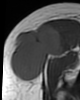
MRI of an extremity soft-tissue mass, one axial slice. Slice 25 of 46 in the series (ordered by position). MR volume resampled by the dataset authors to the PET/CT grid (not the native acquisition matrix). 3.27 mm slice thickness. 80 × 100 image matrix, field of view 78 × 98 mm. Female patient. From the clinical record (not read from this slice): histological type: synovial sarcoma; grade: intermediate; site of the primary tumour: right thigh.
Structures marked on this image (expert contour drawn on MRI and transferred to this co-registered scan by the dataset authors):
- gross tumour volume including surrounding oedema: box from (x=10, y=24) to (x=63, y=82) px
- gross tumour volume (mass): (x=10, y=24)–(x=65, y=82)